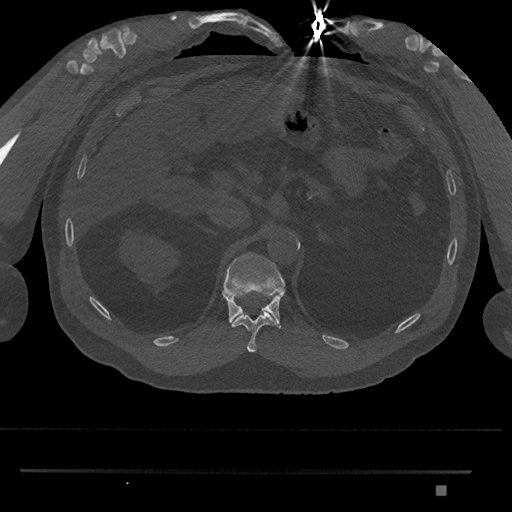
CT including the spine, one axial slice. Position 917 of 1134 along the scan axis. 120 kVp. Bone window (W 1800 / L 400 HU). 512 × 512 image matrix, field of view 429 × 429 mm. Male patient, age 65 years. From the clinical record (not read from this slice): primary cancer: prostate.
Annotated regions visible in this slice (semi-automatic segmentation, software-assisted and operator-edited):
- T11 vertebra: bounding box [x1, y1, x2, y2] px = [231, 312, 276, 352]
- T12 vertebra: [222, 252, 285, 329]